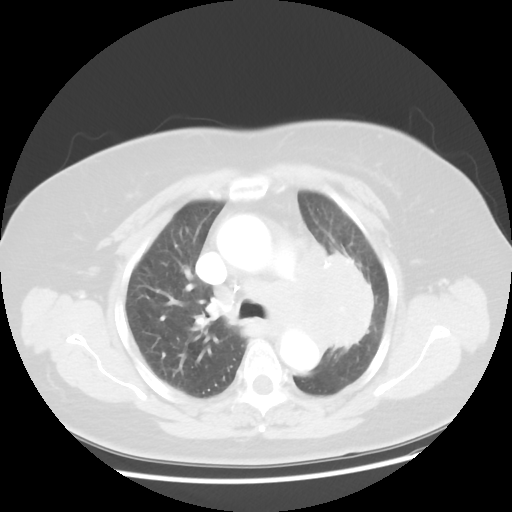
Chest CT, one axial slice. Position 32 of 49 along the scan axis. 120 kVp. Lung window (W 1500 / L -600 HU). 5 mm slice thickness. 512 × 512 image matrix, field of view 374 × 374 mm. Patient: female, 58 years. From the clinical record (not read from this slice): clinical TNM (as recorded): T4 N3 M0.
Annotated regions visible in this slice (bounding box drawn by a radiologist):
- lung tumour (recorded histology: small cell carcinoma): box from (x=269, y=233) to (x=372, y=368) px